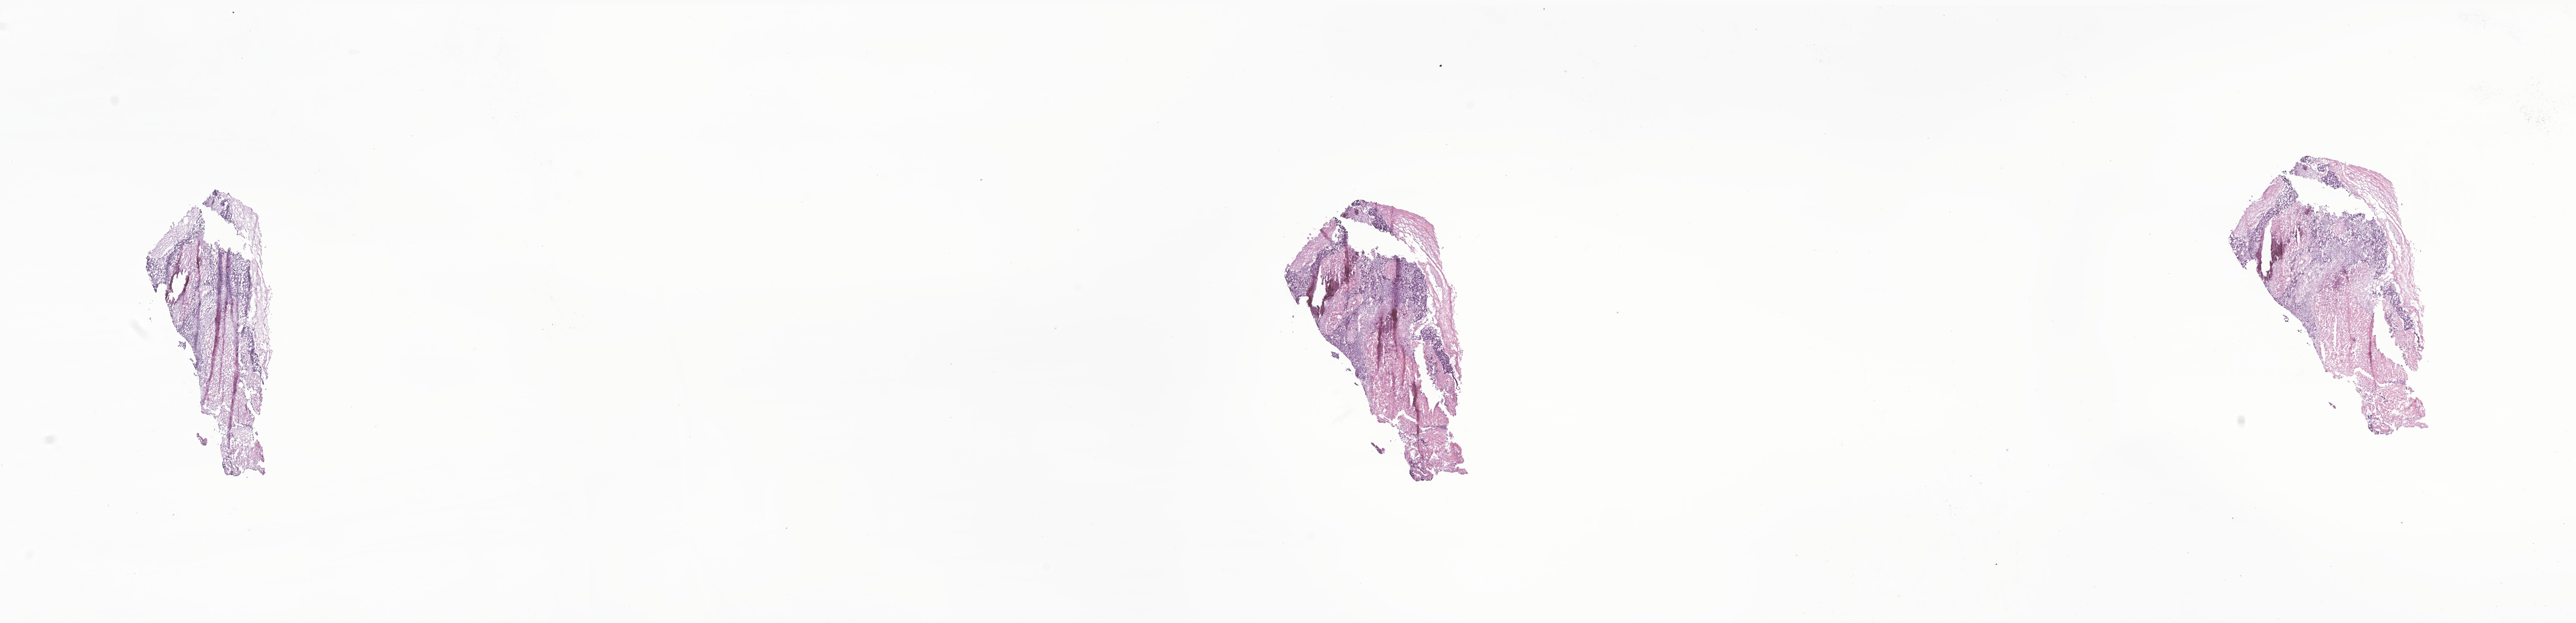
H&E whole-slide image of tumor tissue from the abdomen, low-resolution overview of the scanned area, about 33.7 x 8.2 mm. Frozen section (OCT-embedded). Patient female; age 38 months (3 years 2 months).
• diagnosis (ICD-O-3 morphology term): Neuroblastoma, NOS